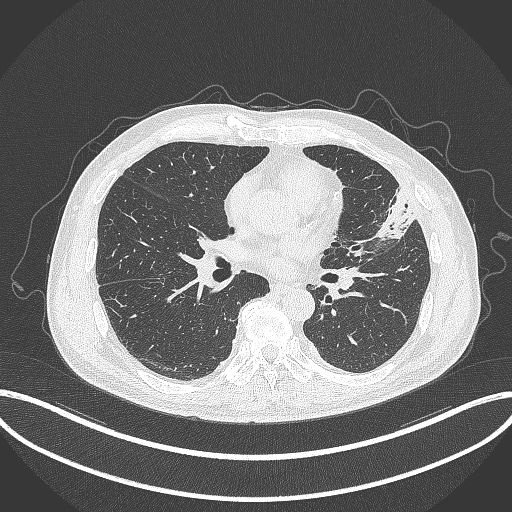
Chest CT, one axial slice; slice 161 of 382 in the series (ordered by position); reconstruction kernel B70f; 120 kVp; lung window (W 1500 / L -600 HU); 1 mm slice thickness; 512 × 512 image matrix, field of view 415 × 415 mm. Patient: male, 64 years. From the clinical record (not read from this slice): clinical TNM (as recorded): T4 N1 M0; histopathological grade: G3.
Outlined on this slice (rectangle marked by the reading radiologist):
- lung tumour (recorded histology: adenocarcinoma): box from (x=373, y=183) to (x=416, y=240) px